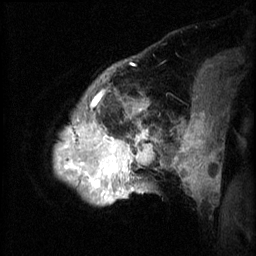
Breast MRI (dynamic contrast-enhanced), one sagittal slice. Position 11 of 60 along the scan axis. 3 images stored at this slice position (order not interpretable as contrast timing). 1.5 T. TE 4.2 ms, TR 8.2 ms. 2.3 mm slice thickness. 256 × 256 image matrix, field of view 200 × 200 mm. Patient: female, 50 years.
Structures marked on this image (semi-automatic segmentation, software-assisted and operator-edited):
- analysis volume of interest (the breast-tissue region the enhancement analysis was run in; not a lesion): box from (x=56, y=64) to (x=169, y=207) px
- tumour enhancement mask (voxels above the 70 % enhancement threshold inside the analysis volume of interest): (x=56, y=100)–(x=155, y=199)